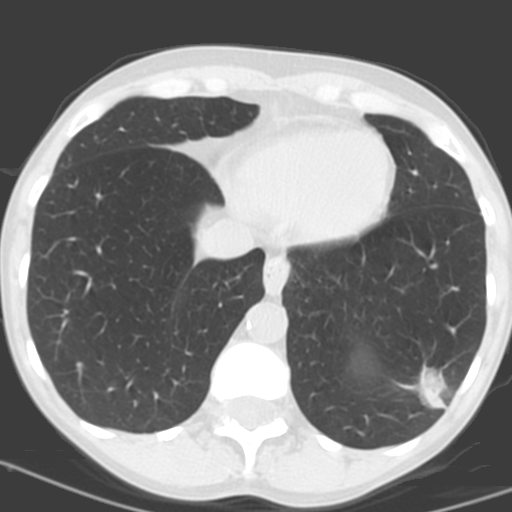
Low-dose screening chest CT, one axial slice. Slice 43 of 156 in the series (ordered by position). 120 kVp. Lung window (W 1500 / L -600 HU). 3.2 mm slice thickness. 512 × 512 image matrix.
Outlined on this slice (outlined manually by an expert reader):
- lesion 1 (tumor, lower lobe of left lung): bounding box (x1, y1, x2, y2) in pixels: (419, 366, 446, 409)